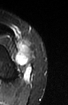
MRI of an extremity soft-tissue mass, one axial slice. Slice 23 of 52 in the series (ordered by position). STIR. MR volume resampled by the dataset authors to the PET/CT grid (not the native acquisition matrix). 3.27 mm slice thickness. 68 × 105 image matrix. Female patient. From the clinical record (not read from this slice): histological type: spindle cell suggestive of biphasic synovial sarcoma; grade: intermediate; site of the primary tumour: left knee.
Structures marked on this image (expert contour drawn on MRI and transferred to this co-registered scan by the dataset authors):
- gross tumour volume including surrounding oedema: bounding box <14,43,34,83> (left, top, right, bottom; pixels)
- gross tumour volume (mass): <14,47,34,83>